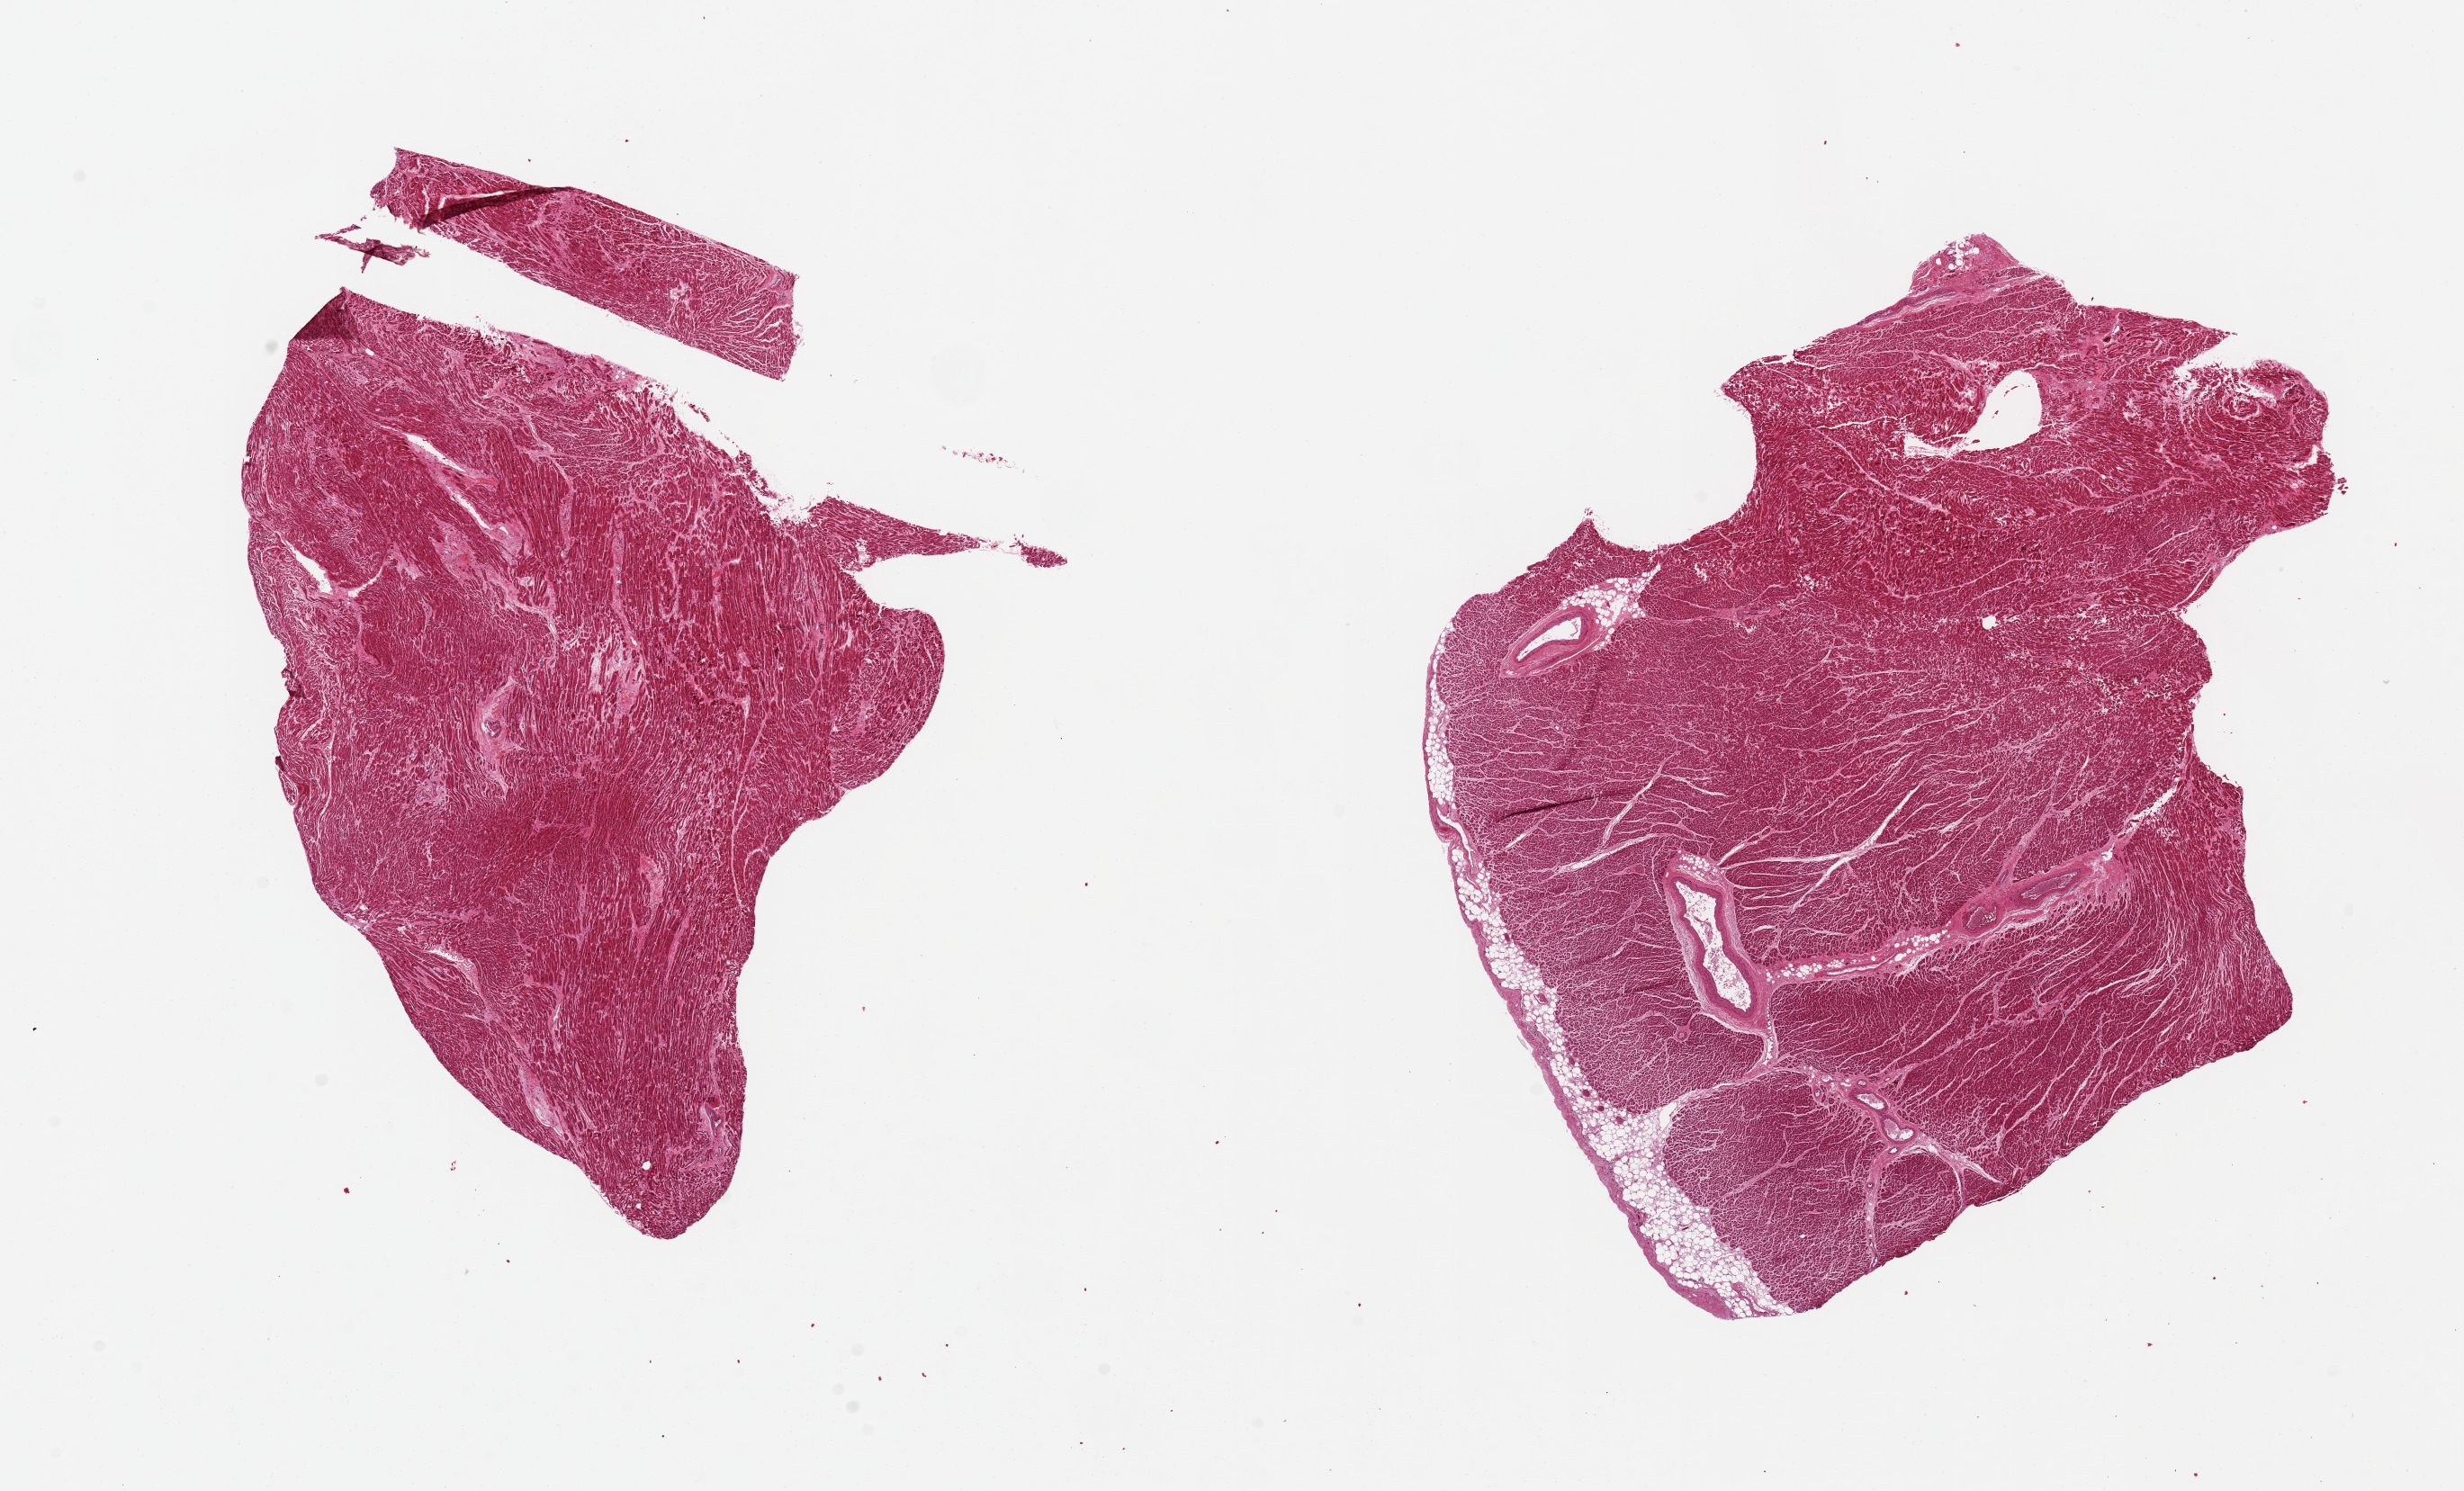
Digitized hematoxylin and eosin (H&E)-stained section, low-resolution overview of the scanned area, about 21.7 x 13.1 mm (acquisition: 20x scan); PAXgene-fixed, paraffin-embedded tissue; section of heart (target tissue); tissue donor sample.
- pathologist's review note for this sample: 2 pieces, 10x7 & 9x7.5mm; Scattered foci of fibrosis. 0.5 mm thick subpericardial adipose on one side of larger piece